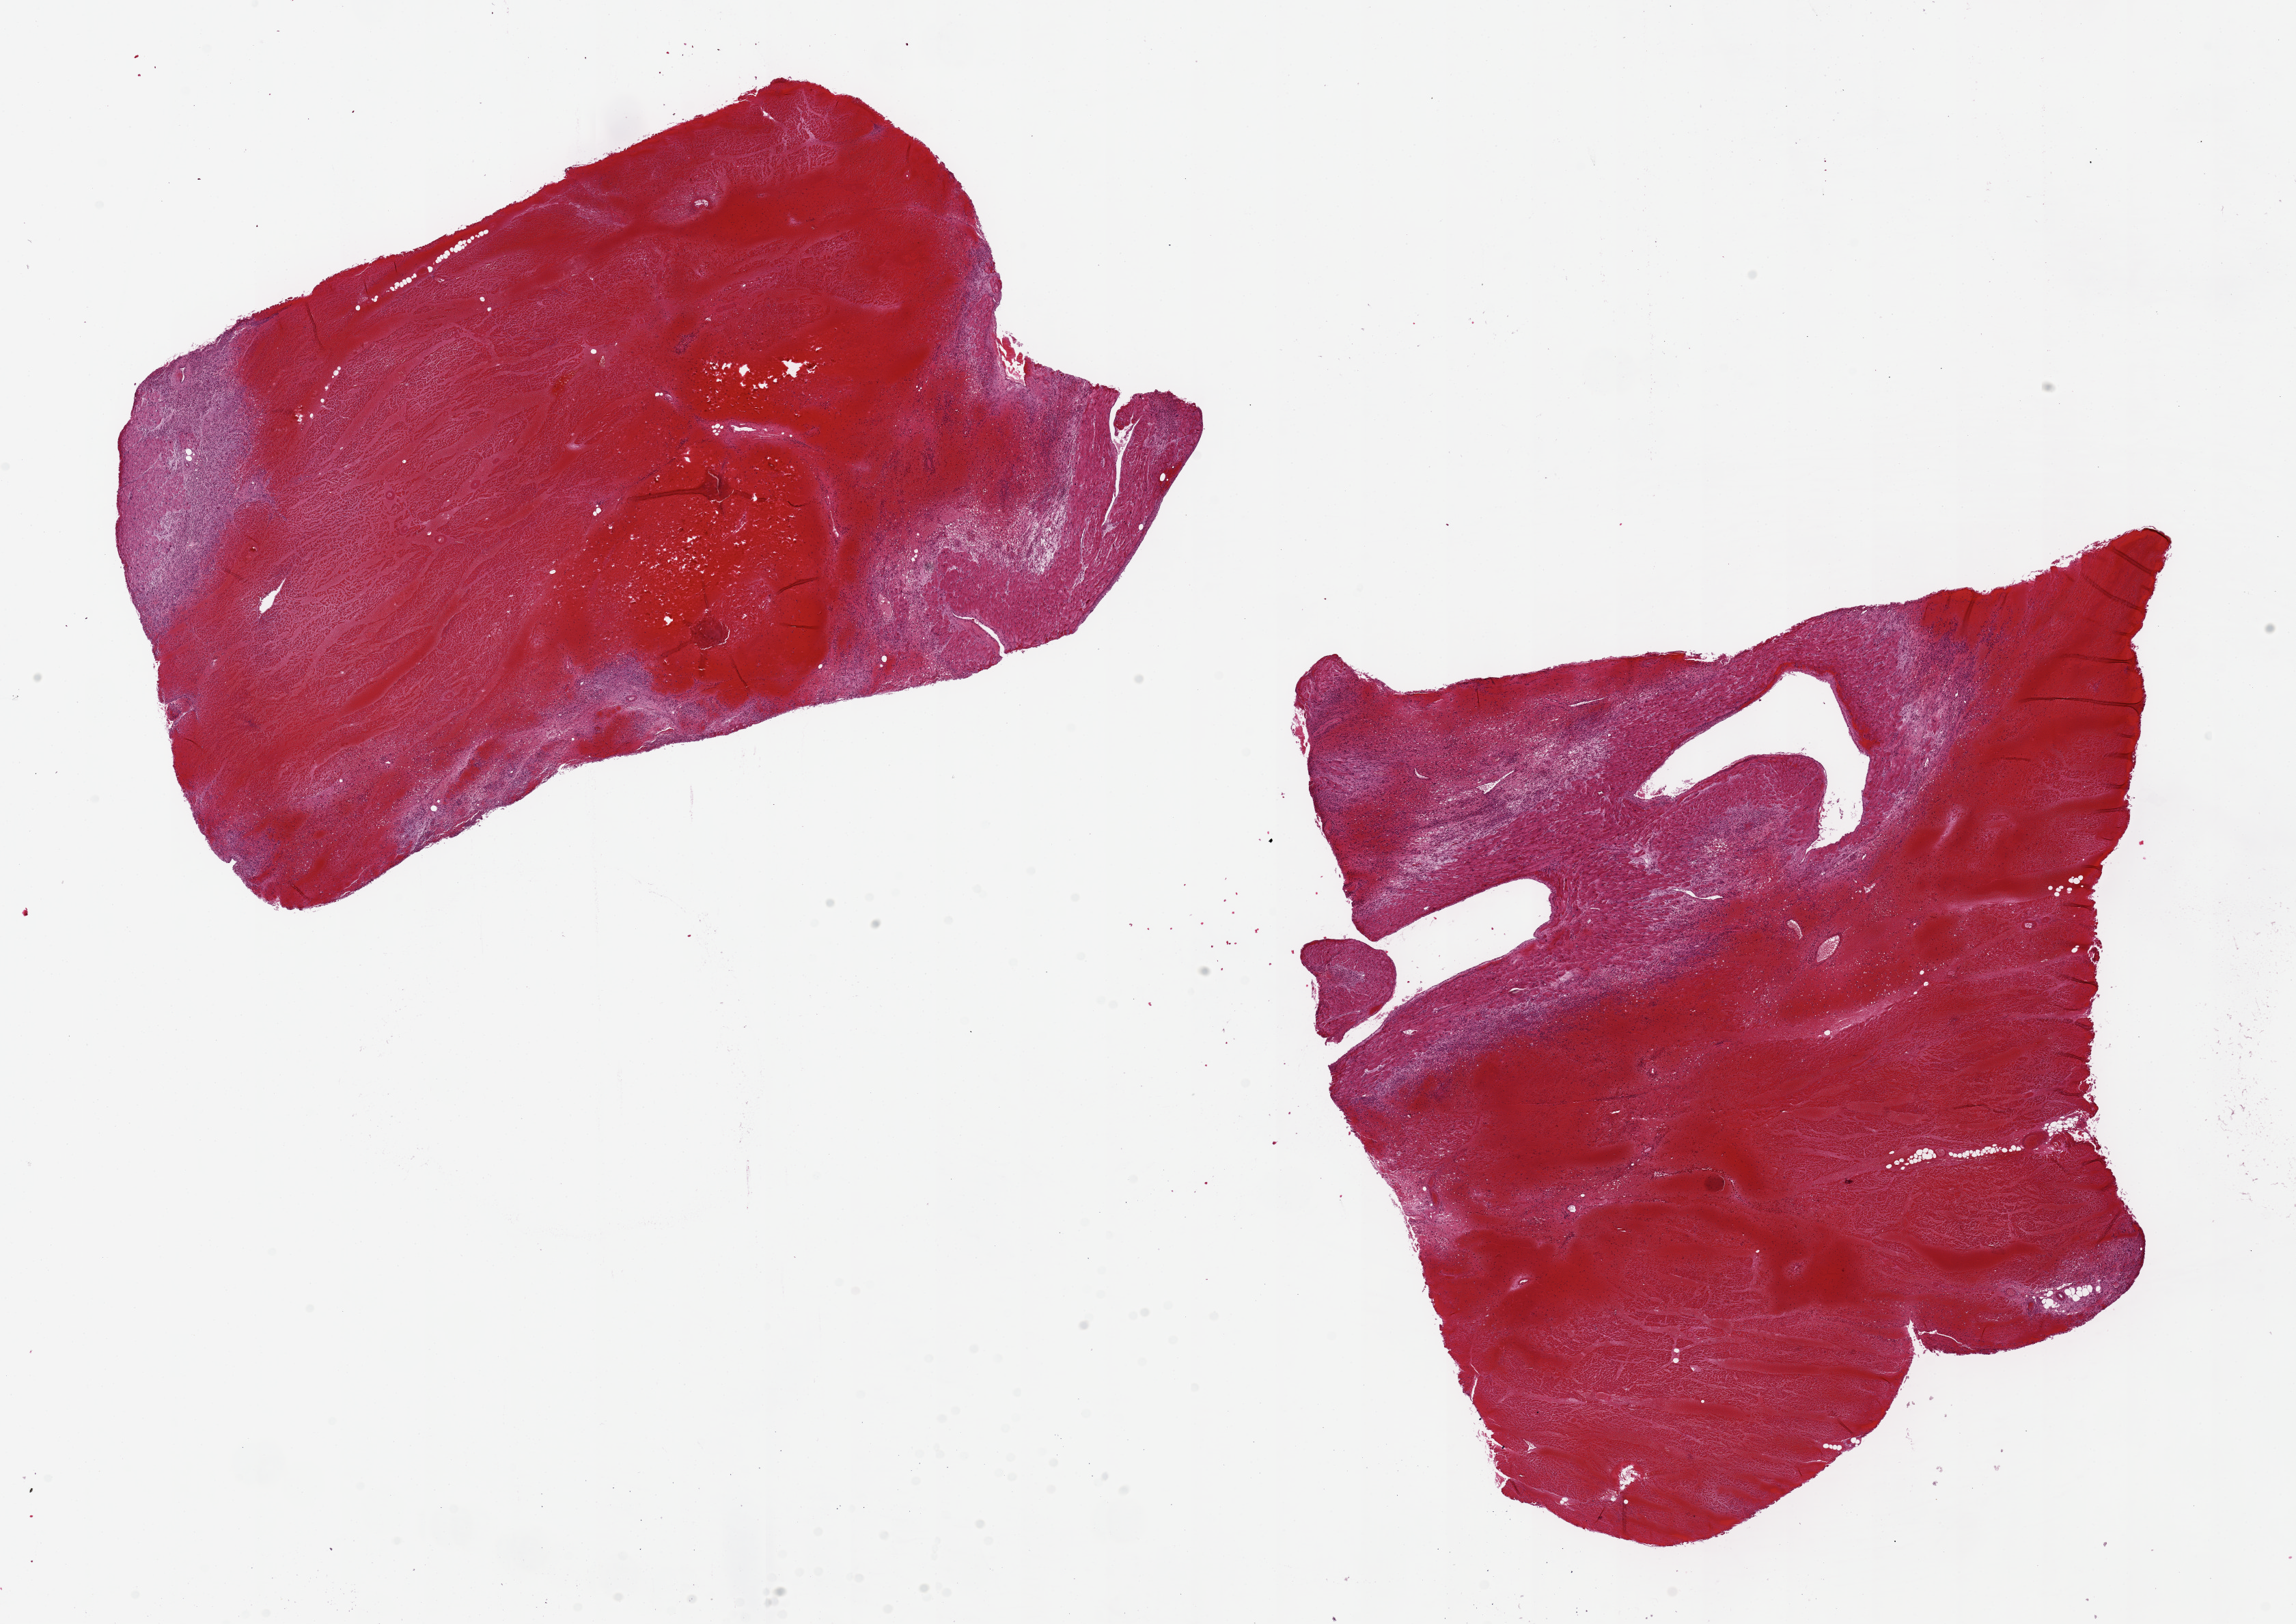
Haematoxylin and eosin whole-slide image, low-resolution overview of the scanned area, about 26.6 x 18.8 mm; PAXgene-fixed, paraffin-embedded tissue; target tissue: heart; donor tissue sample. Donor: male.
Reviewer comment on this tissue sample: 2 pieces, 12x7 & 11x10mm; markedly hemorrhagic, acute/ subacute infarct.